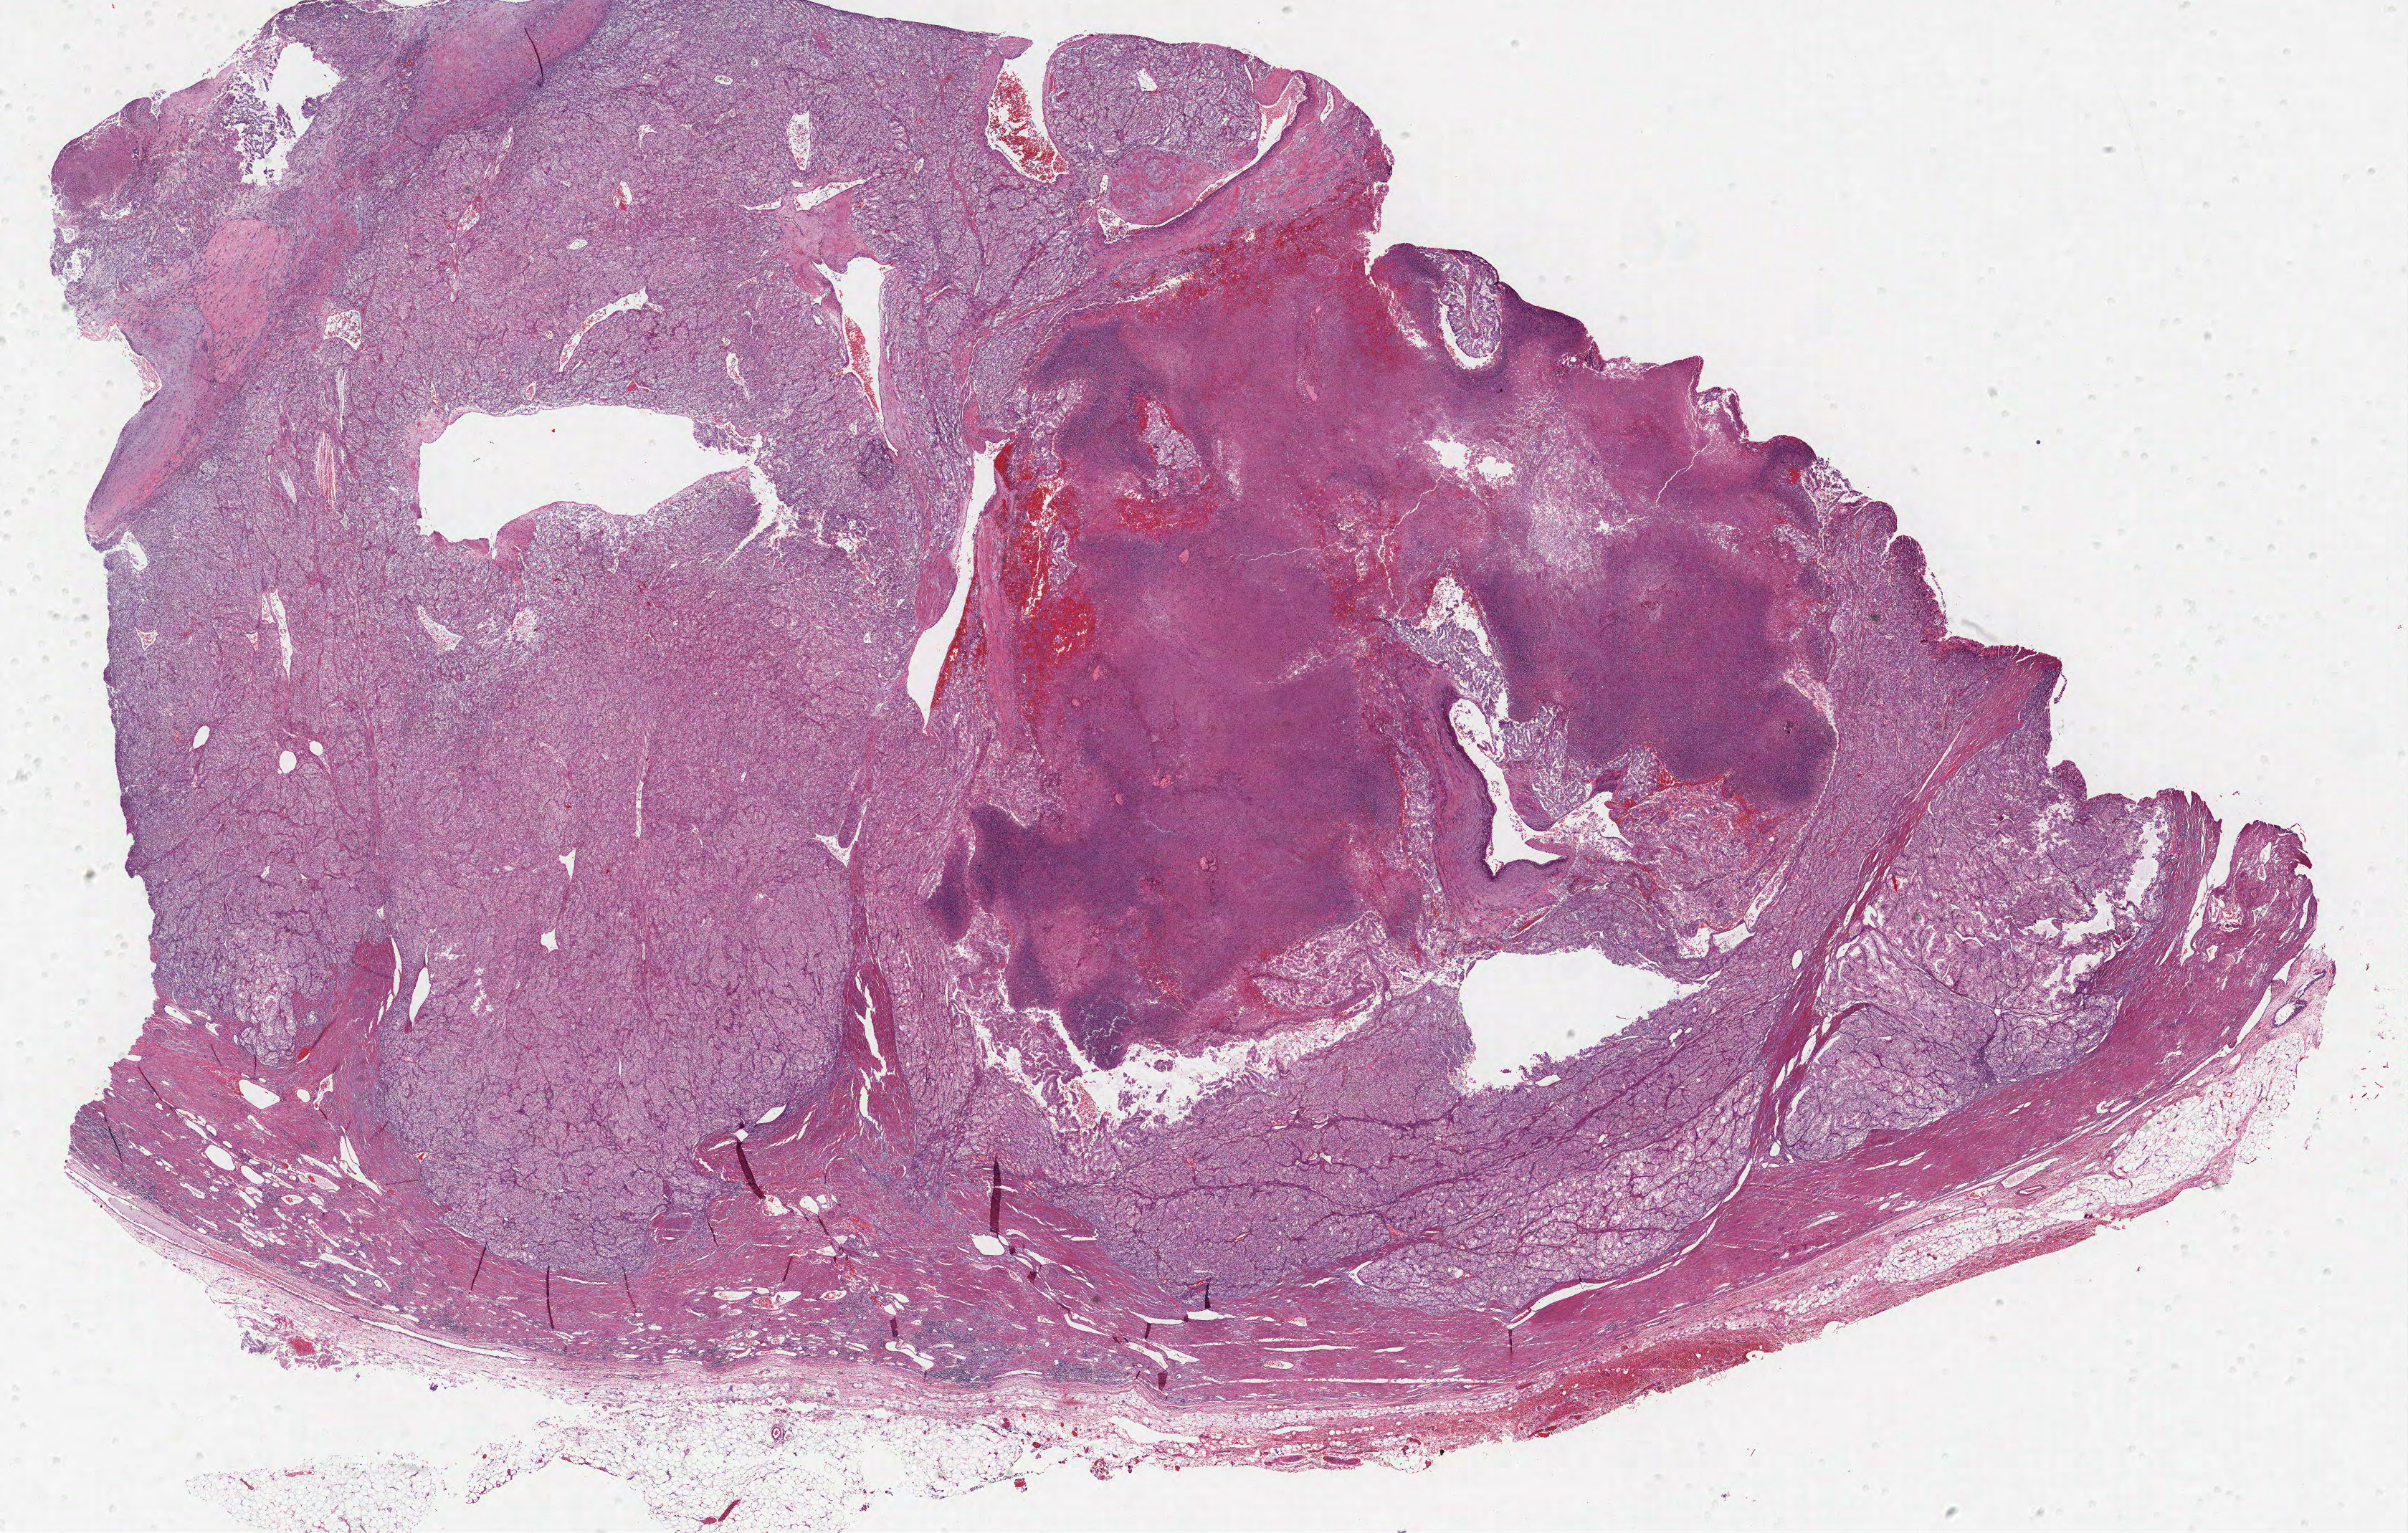
Whole-slide histology image, H&E, shown as a low-resolution overview of the whole scanned area (about 26.9 x 17.1 mm, from a 40x scan). Formalin-fixed paraffin-embedded (FFPE) diagnostic section. Sample: primary tumour, kidney. Patient: male, age at initial diagnosis 72 years.
Diagnosis: Clear cell adenocarcinoma, NOS.